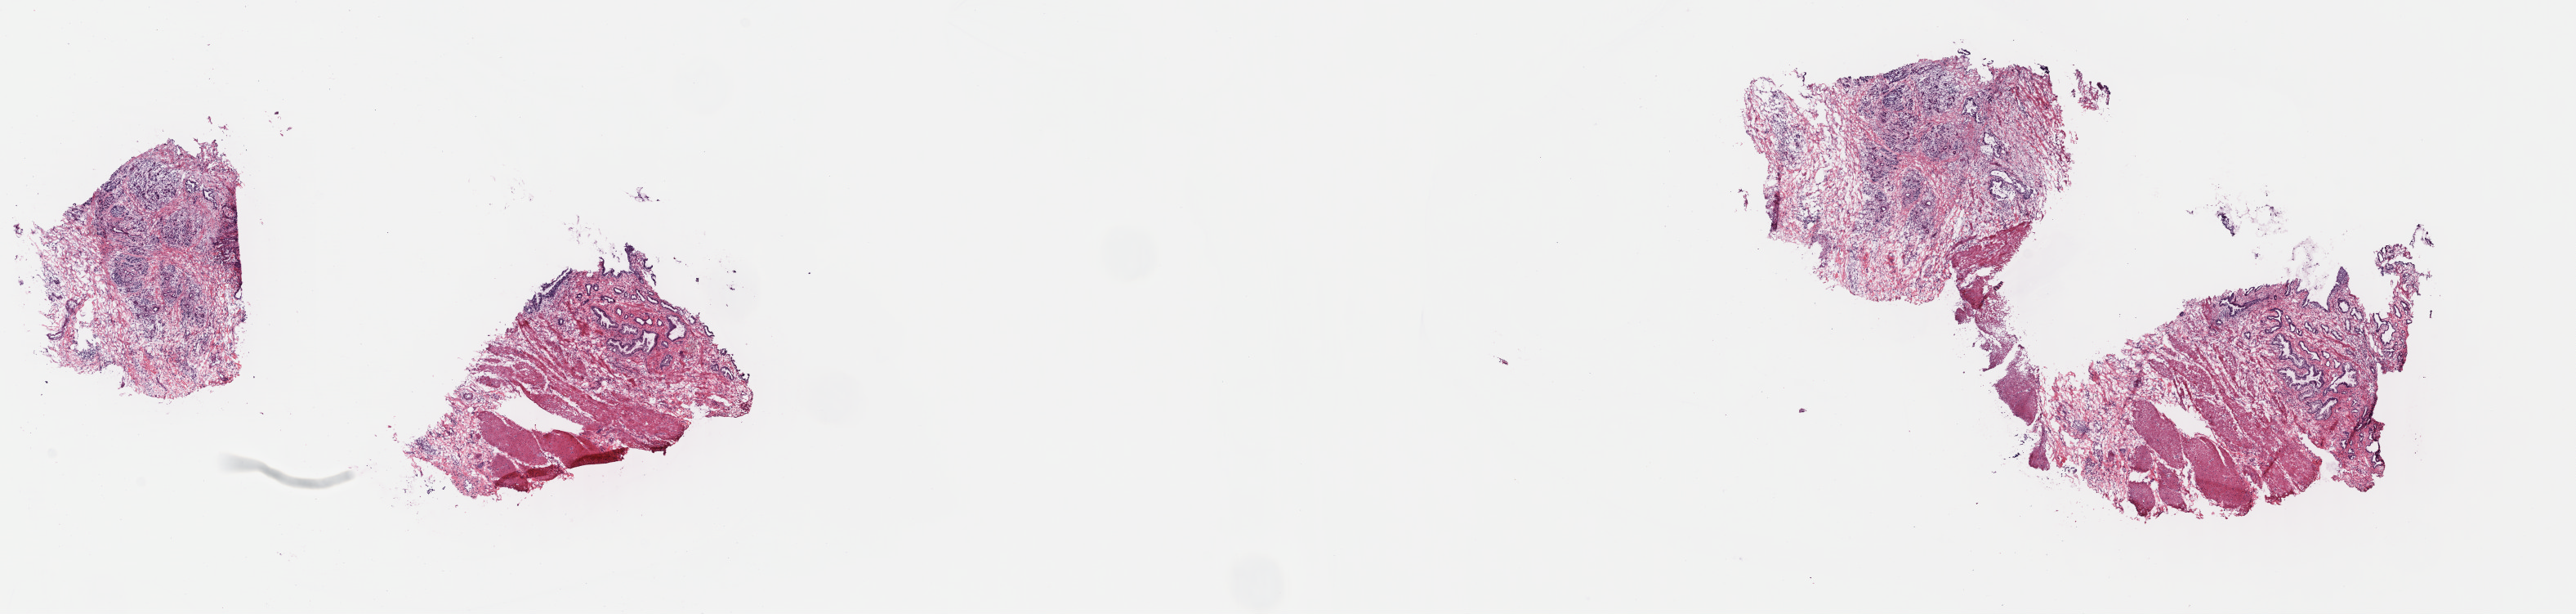
Digitized Hematoxylin and eosin (H&E) stained tissue section (whole slide), low-resolution overview of the scanned area, about 24.8 x 5.9 mm (acquisition: 40x scan). Frozen section from the top of the tissue portion. Sample: primary tumour, pancreas. Male, age 77 years at initial diagnosis. Histologic grade: G1 (well differentiated). Composition of this section per pathologist review: tumour cells 35%, tumour nuclei 15%, normal cells 65%, stromal cells 0%, necrosis 0%. Infiltration values recorded for this section: lymphocyte infiltration 4%, monocyte infiltration 0%, neutrophil infiltration 0%.
Lymph nodes positive (case pathology): 1 of 21 examined. Pathologic diagnosis: Adenocarcinoma, NOS (head of pancreas). AJCC pathologic stage: IIB (7th edition).